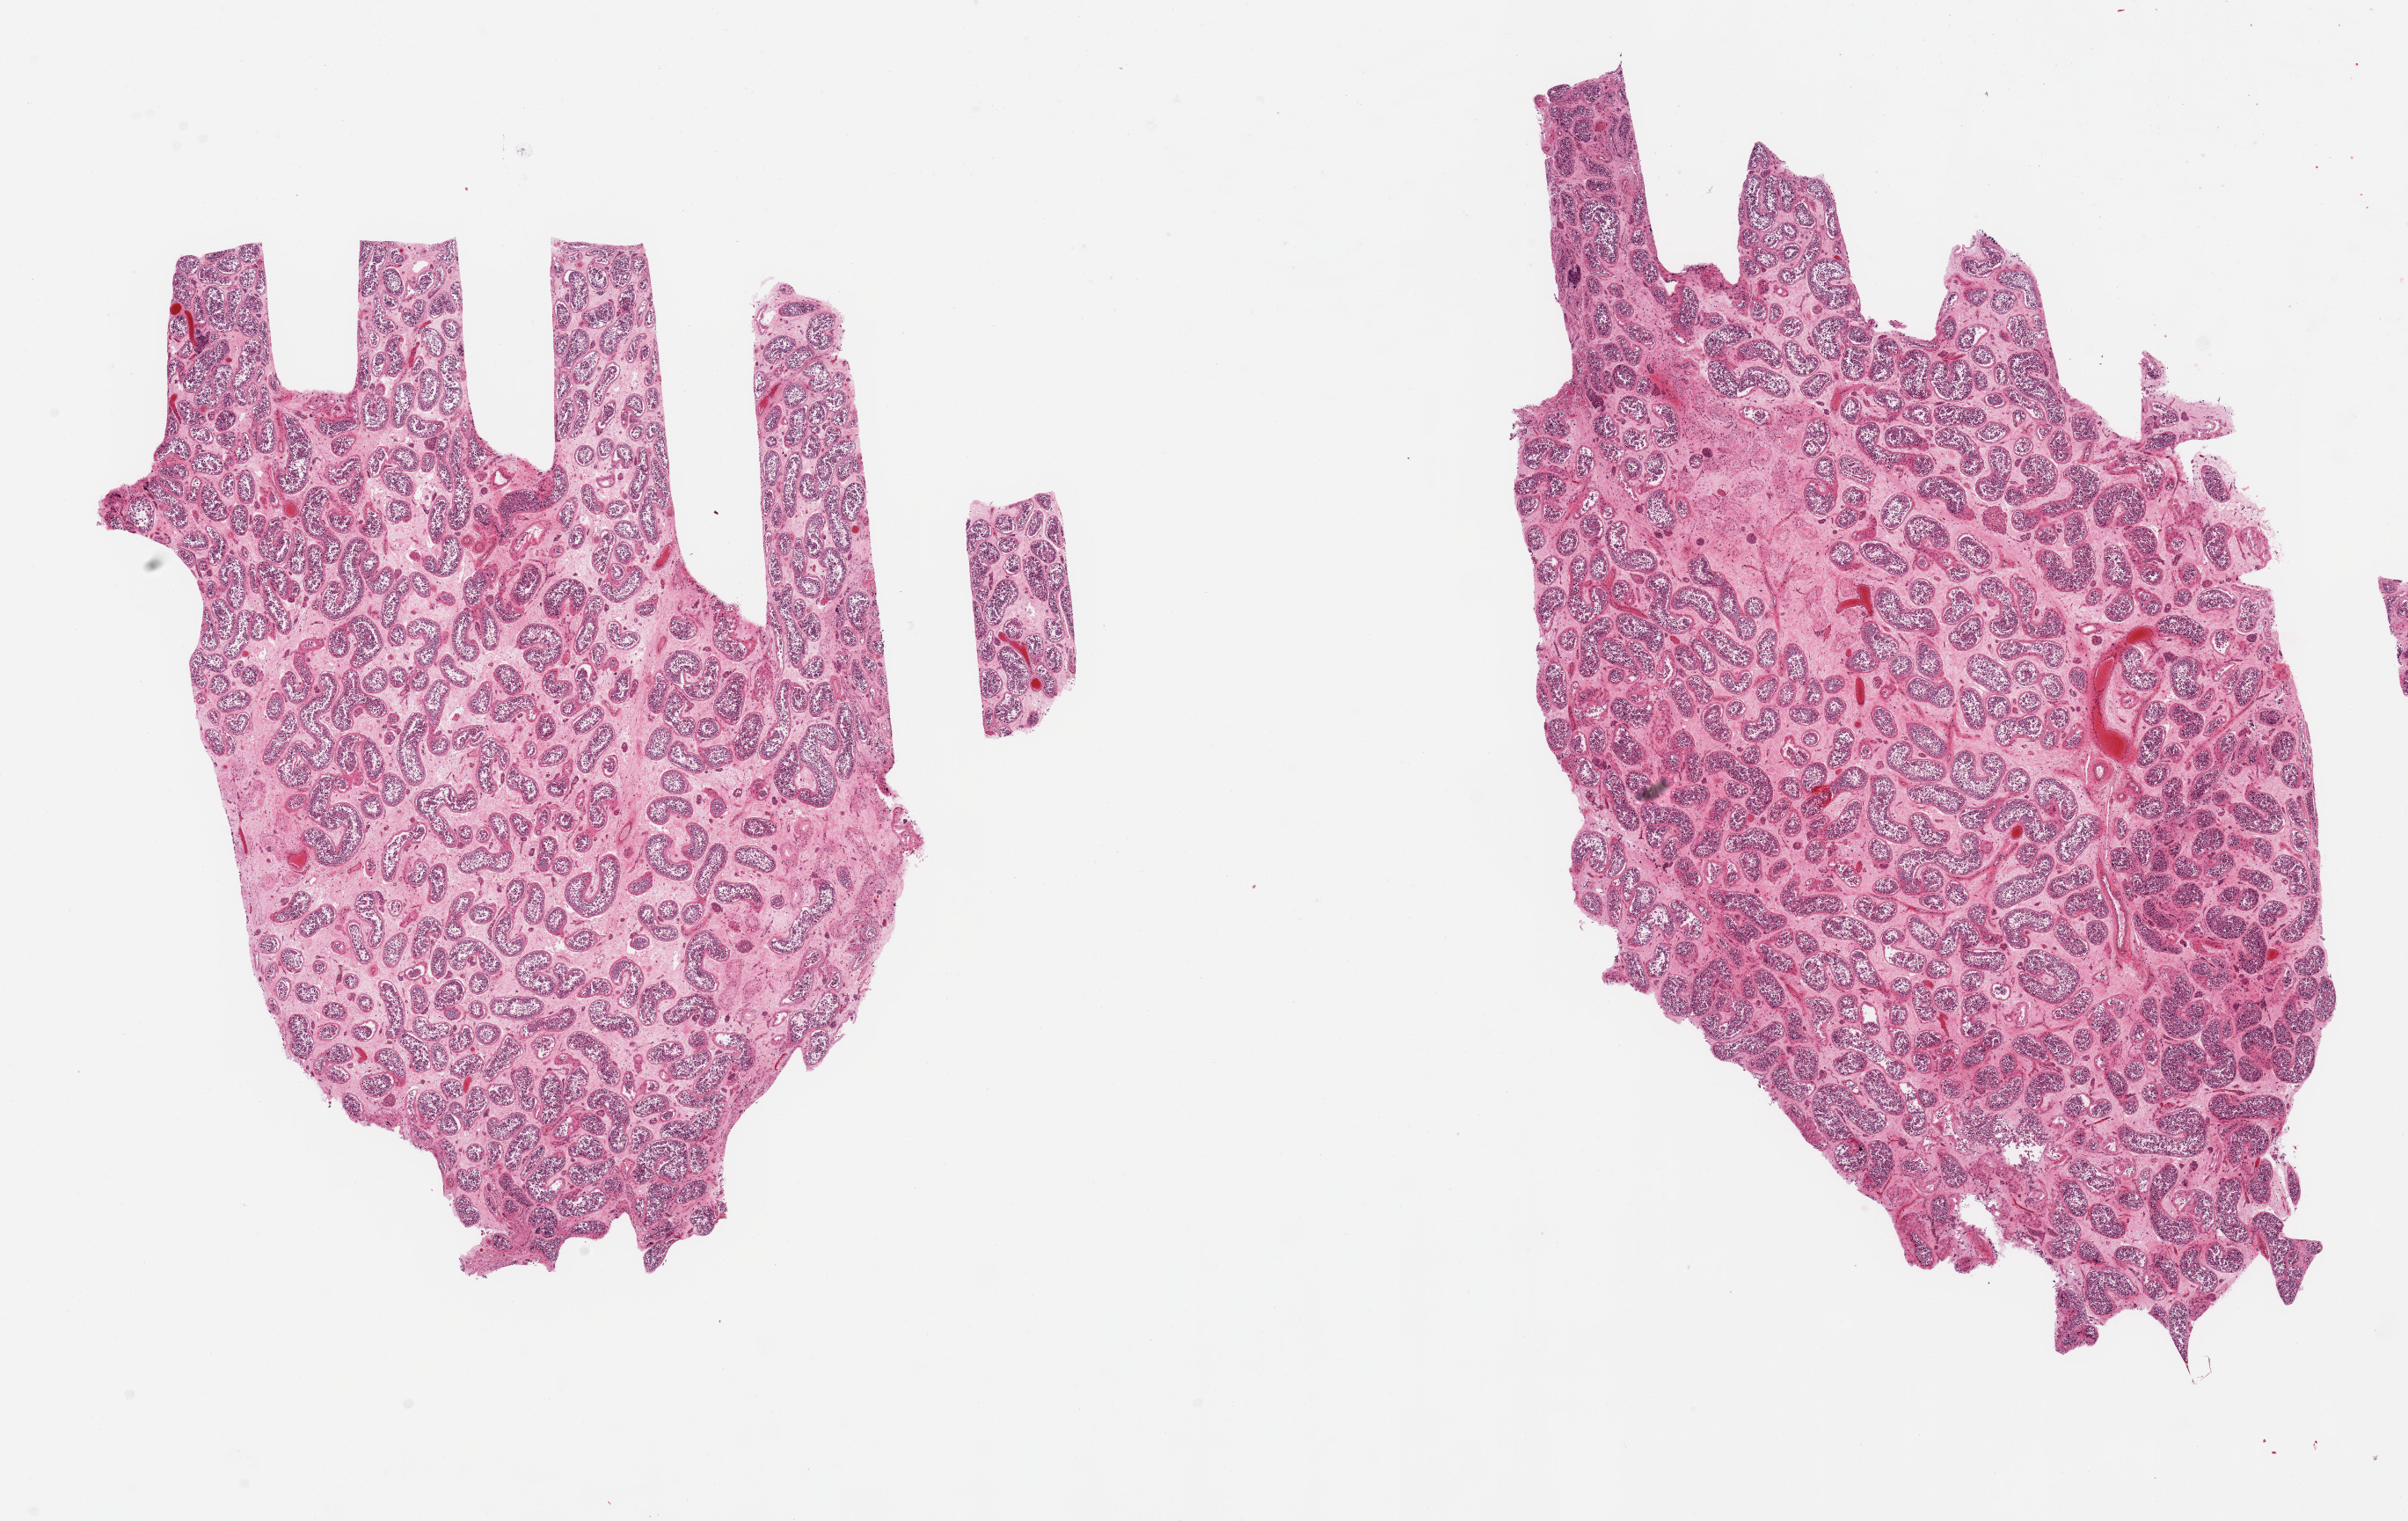
Haematoxylin and eosin whole-slide image — shown as a low-resolution overview of the whole scanned area (about 21.7 x 13.7 mm), PAXgene-fixed paraffin-embedded (PFPE) section, sampled site (target tissue): testis, donor tissue sample. Donor: male.
Reviewer comment on this tissue sample: 2 pieces, spermatogenesis appears reduced; interstitial edema.